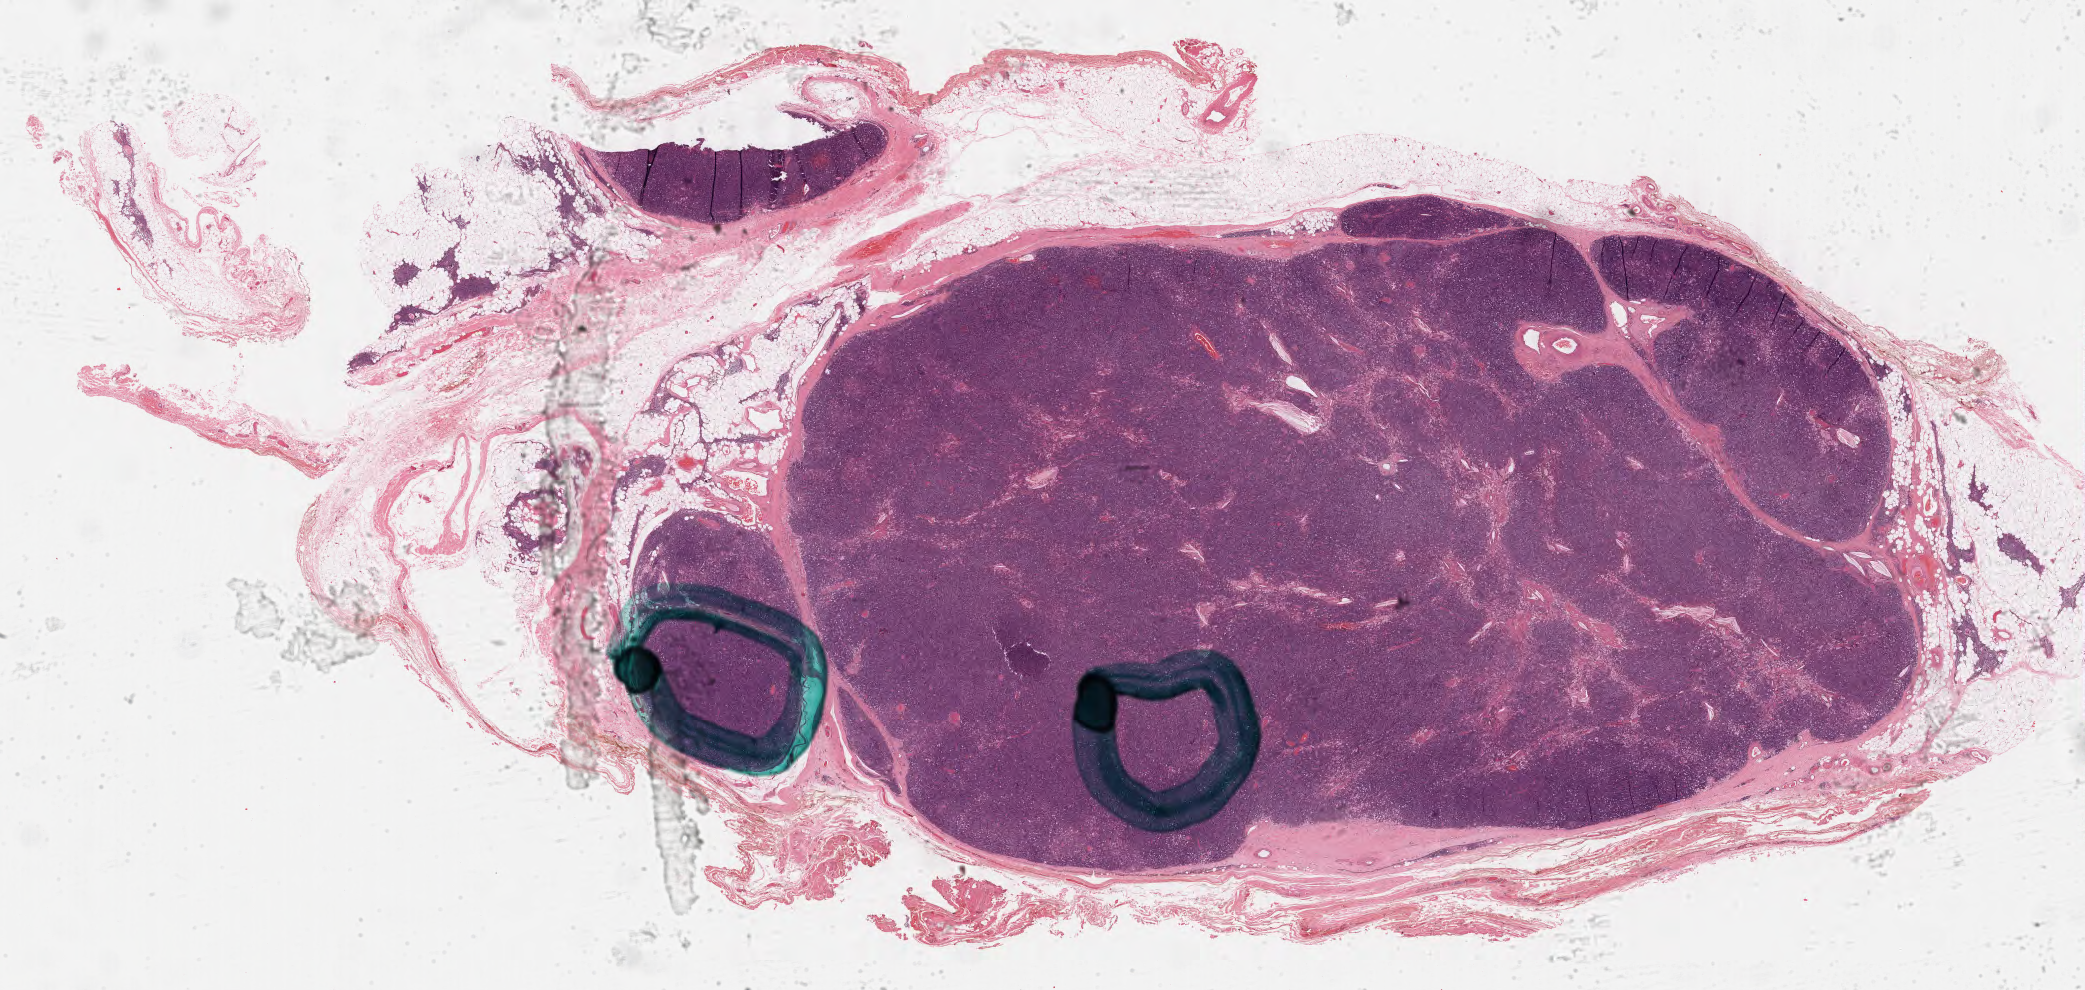
Whole-slide histology image, H&E-stained, a low-resolution overview of the entire scanned area, about 32.9 x 15.6 mm. Formalin-fixed paraffin-embedded (FFPE) diagnostic section. Primary tumour sample from the thymus. Male, age 37 years at initial diagnosis.
Pathologic diagnosis: Thymoma, type B2, malignant.